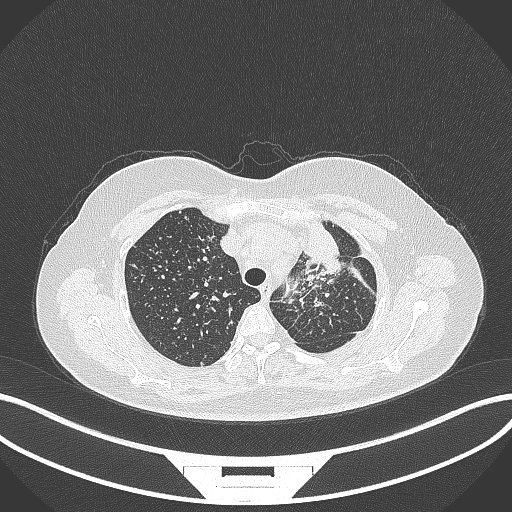
Chest CT, one axial slice; slice 264 of 348 in the series (ordered by position); reconstruction kernel B70f; 120 kVp; lung window (W 1500 / L -600 HU); 512 × 512 image matrix, field of view 400 × 400 mm. Female patient, age 49 years. From the clinical record (not read from this slice): clinical TNM (as recorded): T1c N0 M1.
Structures marked on this image (rectangle marked by the reading radiologist):
- lung tumour (recorded histology: adenocarcinoma): bounding box (x1, y1, x2, y2) in pixels: (298, 215, 349, 277)